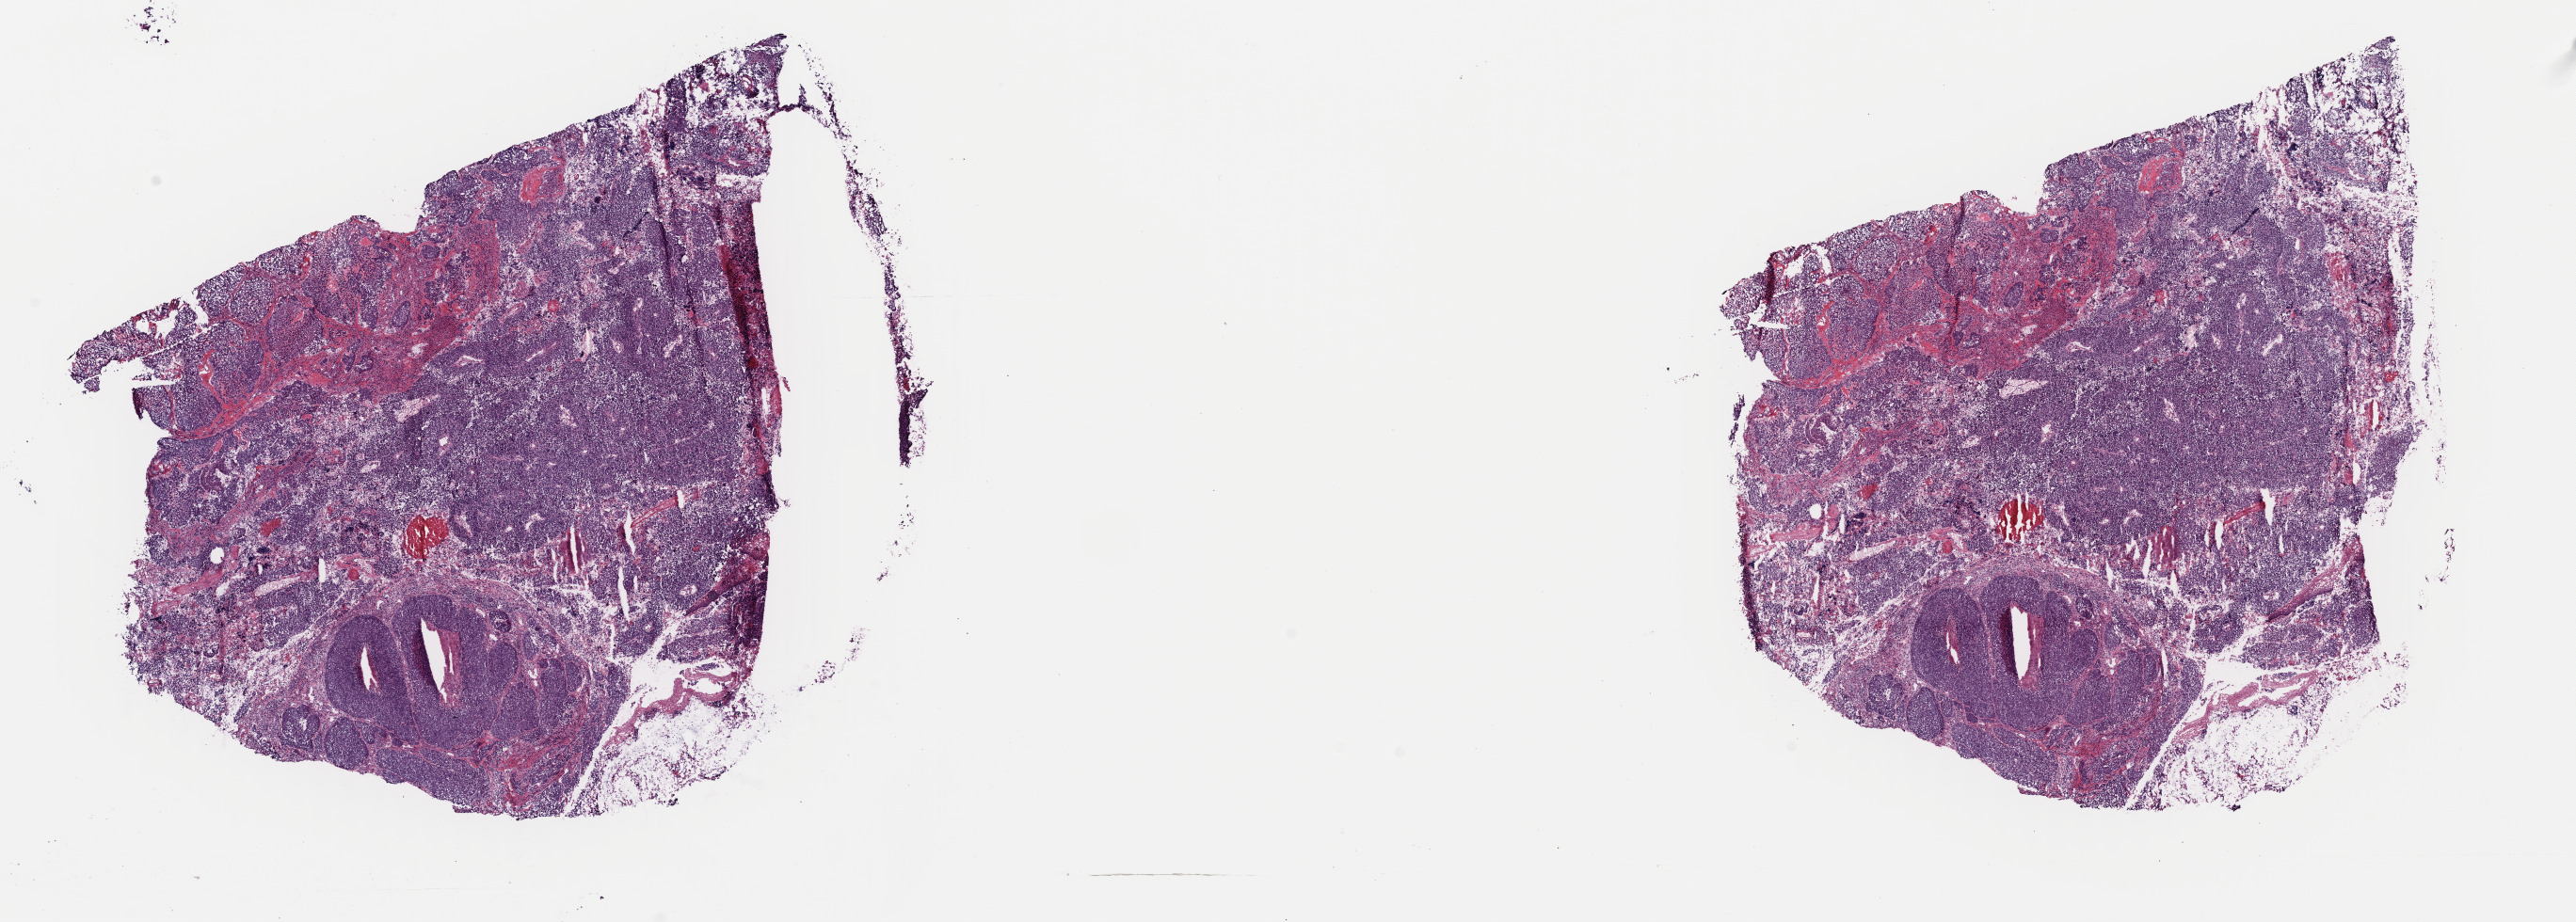
Whole-slide histology image, Hematoxylin and eosin (H&E) stained, whole scanned area (about 21.6 x 7.7 mm, from a 40x scan) shown as a low-resolution overview. Frozen section from the top of the tissue portion. Sample: primary tumour, cervix. Patient: female, age at initial diagnosis 45 years.
Diagnosis: Adenocarcinoma, endocervical type.